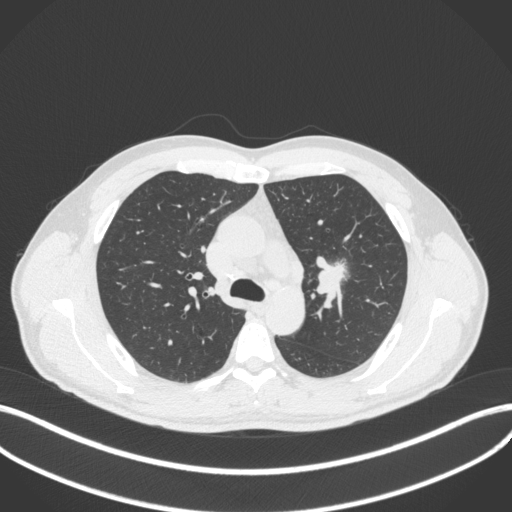
Chest CT, one axial slice; slice 287 of 383 in the series (ordered by position); 120 kVp; lung window (W 1500 / L -600 HU); 512 × 512 image matrix, field of view 400 × 400 mm. Patient: male, 50 years. Case-level facts recorded for this patient, not image findings: clinical TNM (as recorded): T1c N1 M1b.
Outlined on this slice (bounding box drawn by a radiologist):
- lung tumour (recorded histology: squamous cell carcinoma): box from (x=313, y=257) to (x=351, y=297) px